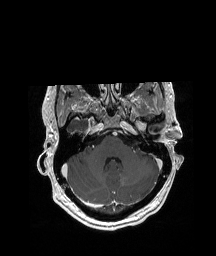
Brain MRI from a brain-tumour surgery series, one axial slice; position 147 of 208 along the scan axis; T1-weighted post-contrast; 1 mm slice thickness; 216 × 256 image matrix, field of view 228 × 270 mm. Case-level facts recorded for this patient, not image findings: histopathology: Glioblastoma; WHO grade: 4; IDH mutation: no; tumour location: Left Anterior/Superior Temporal.
Structures marked on this image (outlined manually by an expert reader):
- tumour: bounding box (x1, y1, x2, y2) in pixels: (124, 114, 132, 125)